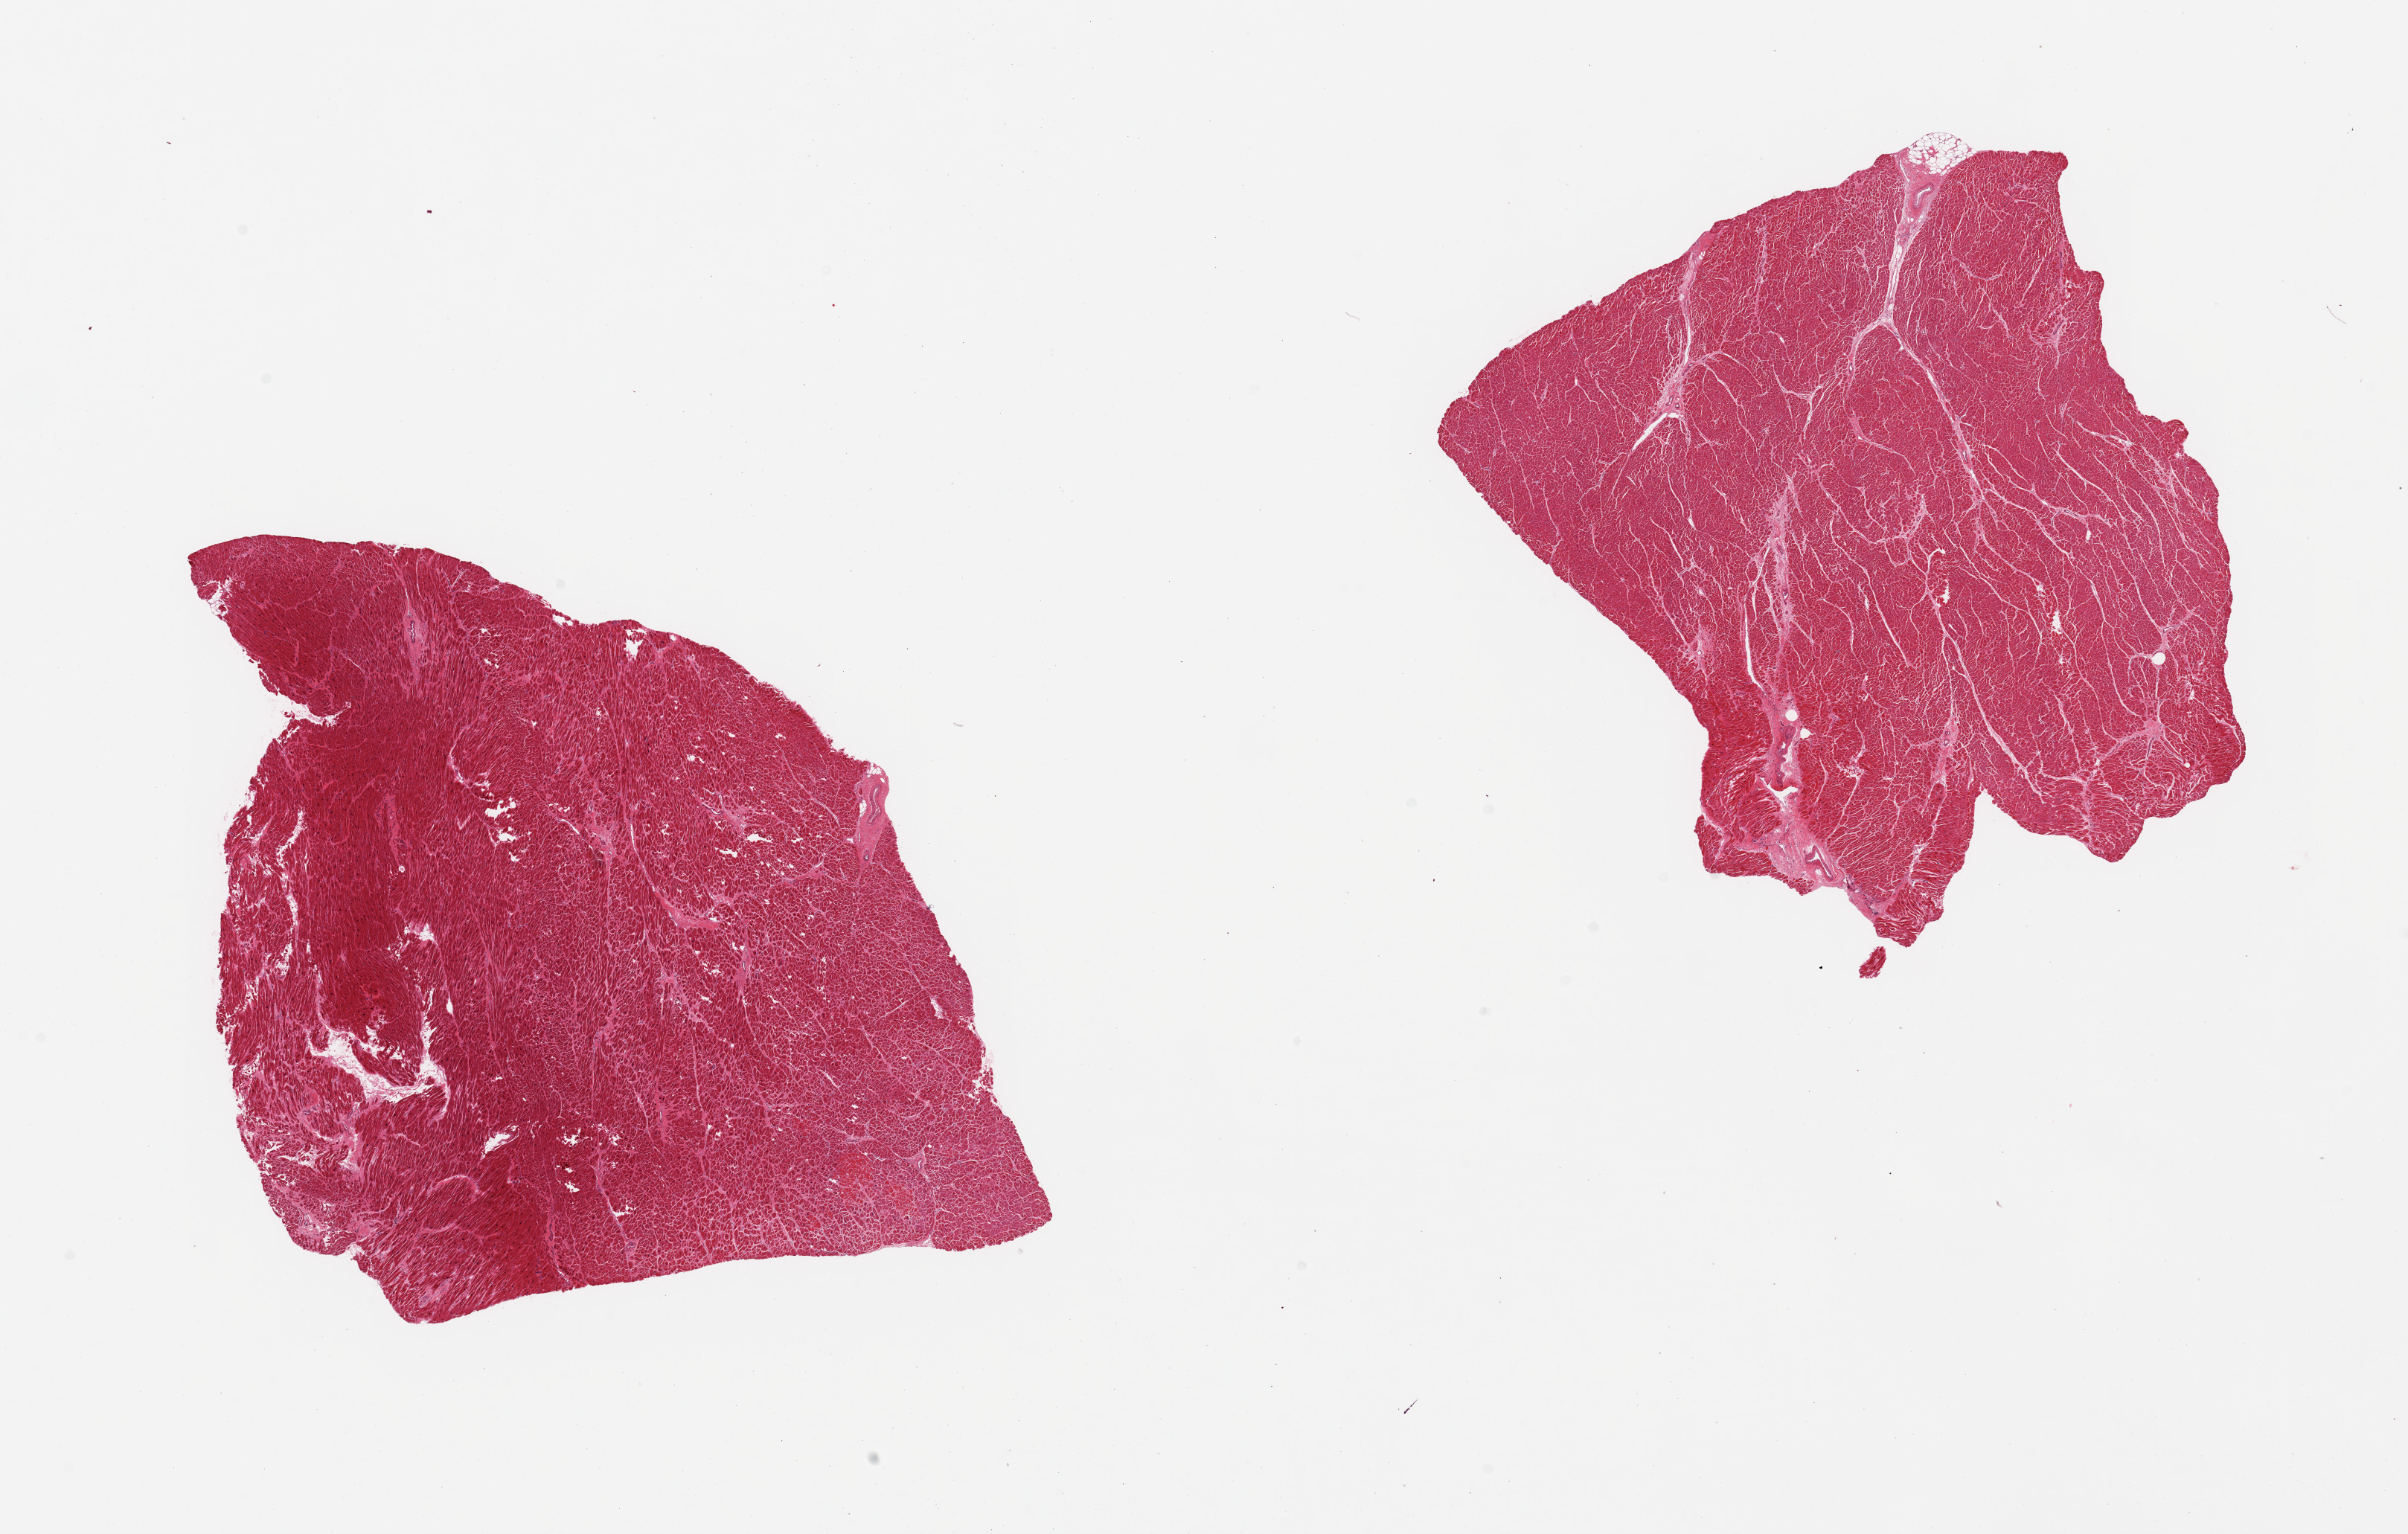
H&E whole-slide image, low-resolution overview of the scanned area, about 25.6 x 16.3 mm (acquisition: 20x scan). PAXgene-fixed paraffin-embedded (PFPE) section. Target tissue: heart. Donor tissue sample. Donor sex: male.
• reviewer comment on this tissue sample: 2 pieces